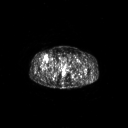
FDG PET of an extremity soft-tissue mass (from a PET/CT study), one axial slice. Position 308 of 311 along the scan axis. 128 × 128 image matrix, field of view 700 × 700 mm. Patient: male, 56 years. Case-level facts recorded for this patient, not image findings: histological type: pleiomorphic leiomyosarcoma; grade: intermediate; site of the primary tumour: right thigh.
Outlined on this slice (expert contour drawn on MRI and transferred to this co-registered scan by the dataset authors):
- gross tumour volume including surrounding oedema: bounding box [x1, y1, x2, y2] px = [43, 55, 48, 61]